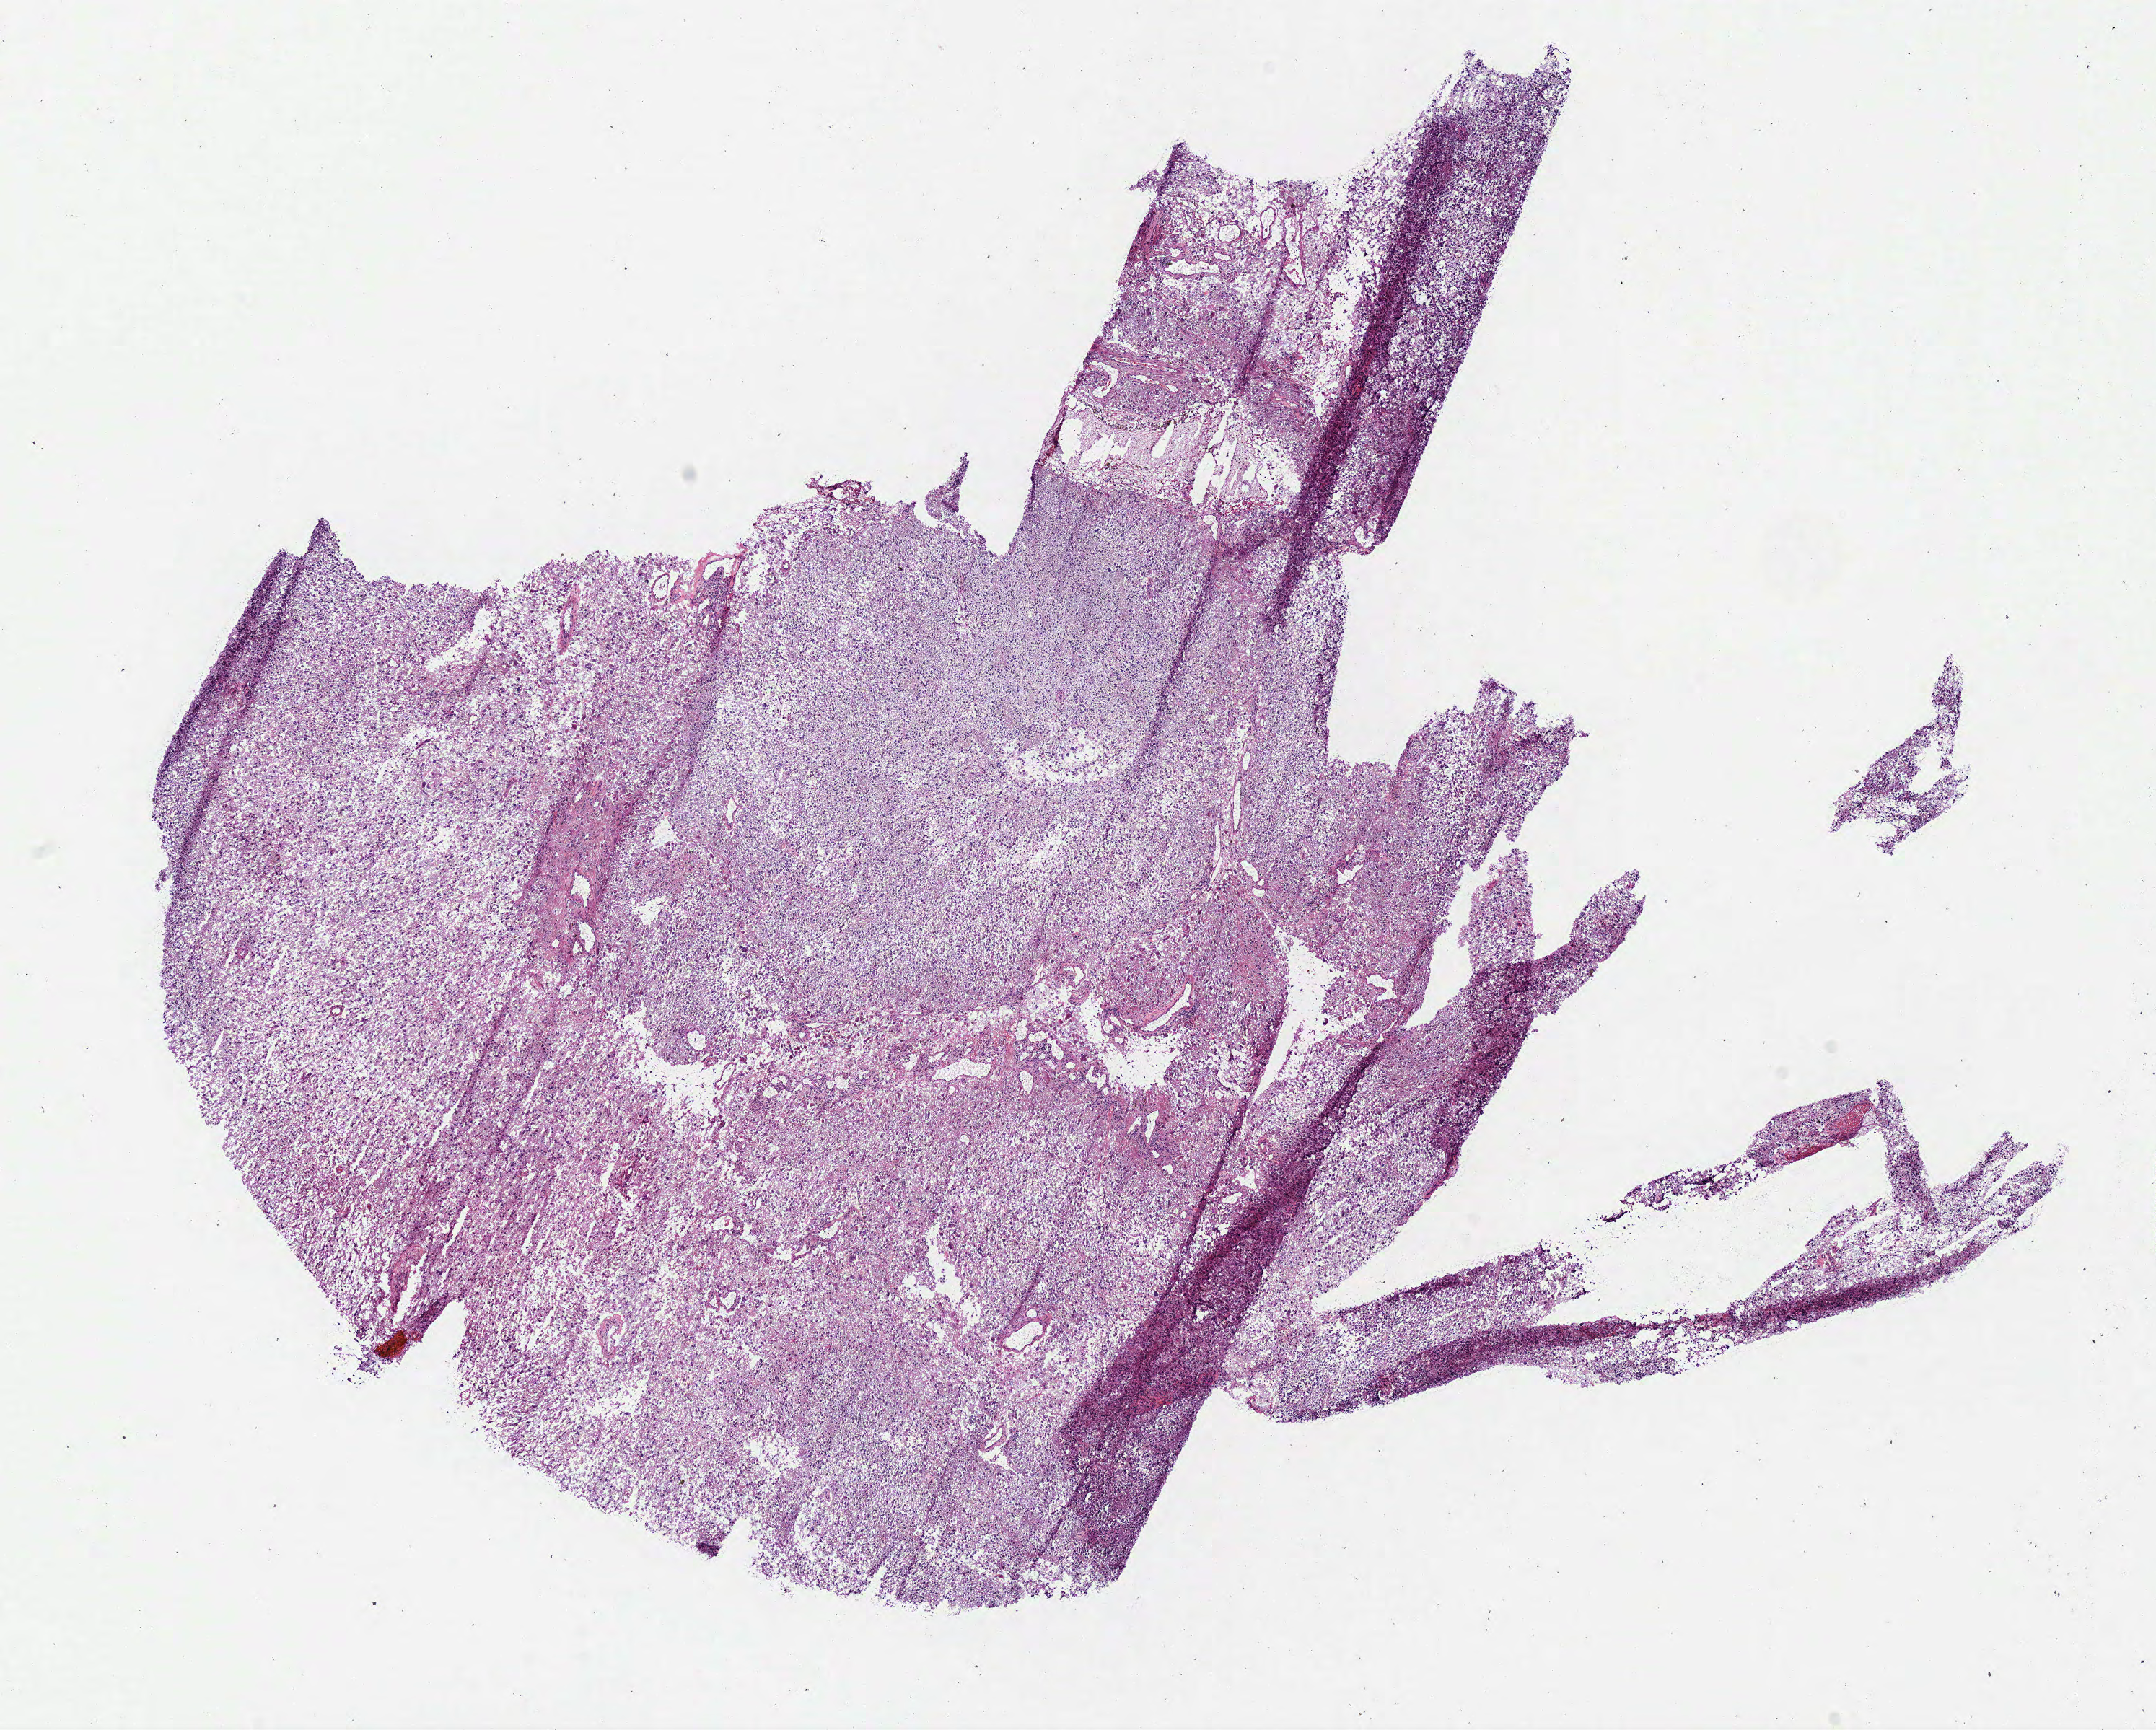
Hematoxylin and eosin (H&E) stained whole-slide image, a low-resolution overview of the entire scanned area, about 11.7 x 9.4 mm (slide scanned at 40x), frozen section from the bottom of the tissue portion, brain, primary tumour sample. Male, age 58 years at initial diagnosis. Pathologist review of this section (percent, as recorded): tumour cells 97%, tumour nuclei 85%, normal cells 0%, stromal cells 3%, necrosis 3%.
• diagnosis: Glioblastoma